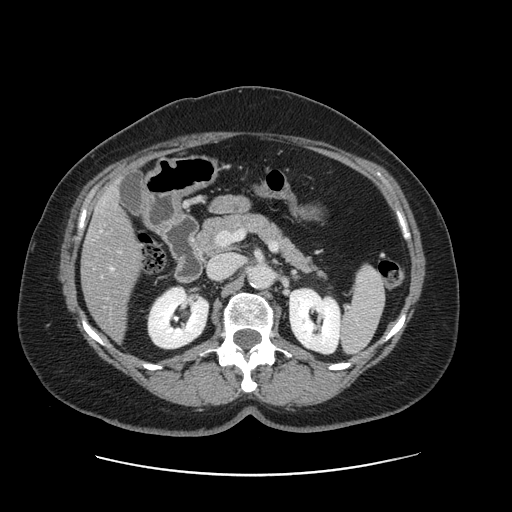
Contrast-enhanced abdominal CT, one axial slice; slice 67 of 161 in the series (ordered by position); 120 kVp; intravenous contrast given; soft-tissue window (W 400 / L 40 HU); 2.5 mm slice thickness; 512 × 512 image matrix, field of view 398 × 398 mm. Female patient, age 62 years. From the clinical record (not read from this slice): diagnosis: colorectal cancer liver metastases, imaged before liver resection; multiple liver metastases: no; largest metastasis: 2.5 cm; chemotherapy before resection: yes.
Annotated regions visible in this slice (expert manual segmentation):
- liver: bounding box [x1, y1, x2, y2] px = [82, 187, 140, 338]
- portal vein (with intrahepatic branches): [111, 268, 113, 270]